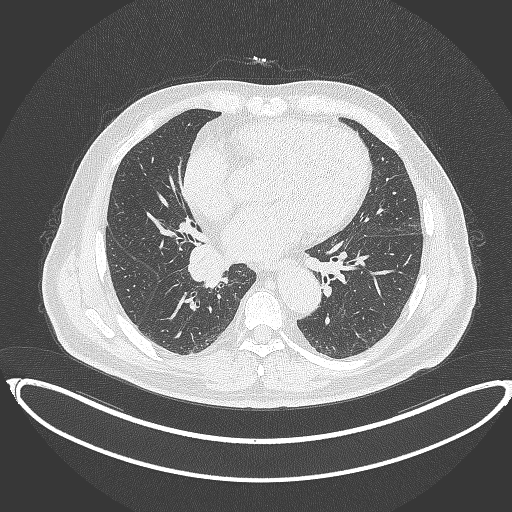
Chest CT, one axial slice; slice 185 of 387 in the series (ordered by position); reconstruction kernel B70f; lung window (W 1500 / L -600 HU); 512 × 512 image matrix, field of view 448 × 448 mm. Male patient, age 61 years. Case-level facts recorded for this patient, not image findings: clinical TNM (as recorded): T1b N1 M0.
Structures marked on this image (bounding box drawn by a radiologist):
- lung tumour (recorded histology: squamous cell carcinoma): bounding box <189,243,228,292> (left, top, right, bottom; pixels)